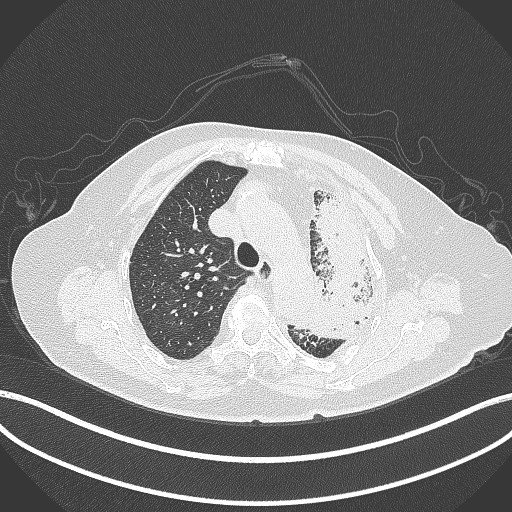
Chest CT, one axial slice. Position 294 of 399 along the scan axis. Reconstruction kernel B70f. 120 kVp. Lung window (W 1500 / L -600 HU). 1 mm slice thickness. 512 × 512 image matrix. Patient: female, 75 years. Case-level facts recorded for this patient, not image findings: clinical TNM (as recorded): T3 N3 M1.
Structures marked on this image (bounding box drawn by a radiologist):
- lung tumour (recorded histology: adenocarcinoma): box from (x=288, y=181) to (x=369, y=340) px